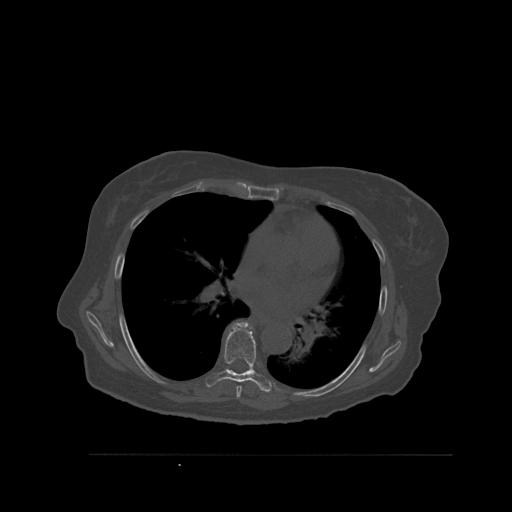
CT including the spine, one axial slice; bone window (W 1800 / L 400 HU); 1.5 mm slice thickness; 512 × 512 image matrix, field of view 470 × 470 mm. Patient: female, 73 years. From the clinical record (not read from this slice): primary cancer: breast.
Structures marked on this image (semi-automatic segmentation, software-assisted and operator-edited):
- T6 vertebra: bounding box (x1, y1, x2, y2) in pixels: (236, 386, 242, 399)
- T7 vertebra: (205, 321, 272, 393)